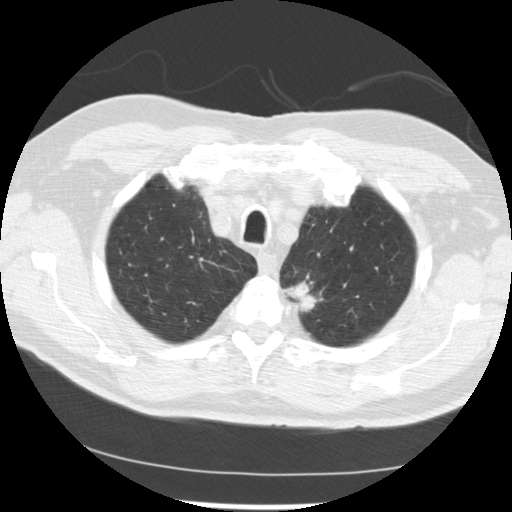
Low-dose screening chest CT, one axial slice. Position 209 of 249 along the scan axis. 120 kVp. Lung window (W 1500 / L -600 HU). 2.5 mm slice thickness. 512 × 512 image matrix.
Structures marked on this image (outlined manually by an expert reader):
- lesion 2 (tumor, upper lobe of left lung): bounding box [x1, y1, x2, y2] px = [287, 281, 319, 312]